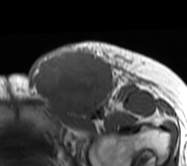
MRI of an extremity soft-tissue mass, one axial slice; slice 35 of 62 in the series (ordered by position); MR volume resampled by the dataset authors to the PET/CT grid (not the native acquisition matrix); 3.27 mm slice thickness; 187 × 166 image matrix. Female patient. Case-level facts recorded for this patient, not image findings: histological type: leiomyosarcoma; grade: high; site of the primary tumour: groin.
Structures marked on this image (expert contour drawn on MRI and transferred to this co-registered scan by the dataset authors):
- gross tumour volume including surrounding oedema: bounding box (x1, y1, x2, y2) in pixels: (29, 40, 151, 120)
- gross tumour volume (mass): (30, 46, 115, 120)